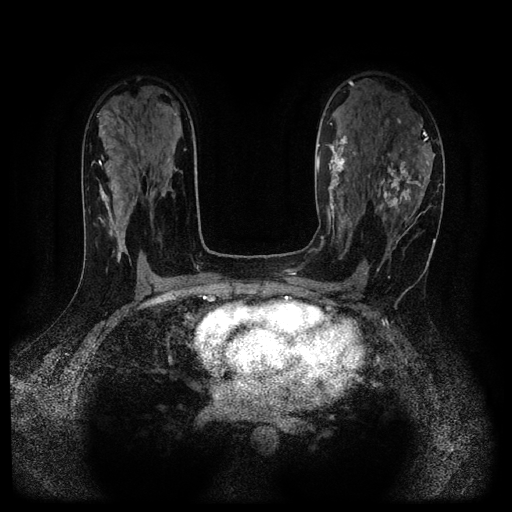
Breast MRI (dynamic contrast-enhanced, multi-phase), one axial slice. Slice 64 of 116 in the series (ordered by position). Dynamic contrast-enhanced series, time point 2 of 5 at this slice position (early post-contrast). 1.5 T. TE 2.7 ms, TR 5.4 ms. 2.2 mm slice thickness. 512 × 512 image matrix, field of view 330 × 330 mm. Patient: female, 43 years.
Annotated regions visible in this slice (semi-automatically segmented with operator editing):
- breast lesion (labelled 'tumour' in the annotation; benign lesions carry a separate 'benign' label): bounding box [x1, y1, x2, y2] px = [367, 153, 426, 223]
- breast lesion (labelled benign in the annotation): [320, 125, 357, 243]